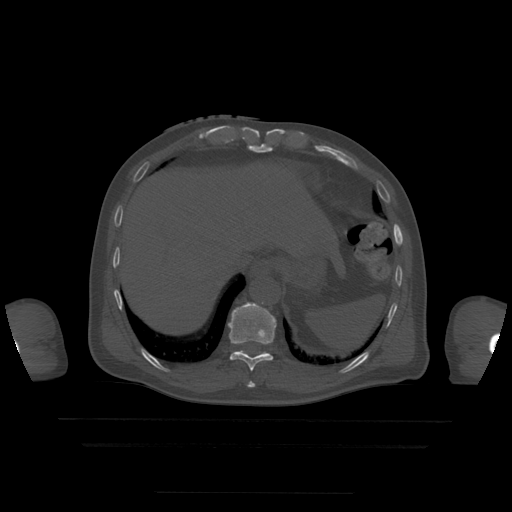
CT including the spine, one axial slice; slice 238 of 522 in the series (ordered by position); bone window (W 1800 / L 400 HU); 512 × 512 image matrix. Patient age 68 years. Case-level facts recorded for this patient, not image findings: primary cancer: urothelial.
Annotated regions visible in this slice (semi-automatic segmentation, software-assisted and operator-edited):
- T10 vertebra: bounding box [x1, y1, x2, y2] px = [228, 302, 277, 372]
- T9 vertebra: [248, 382, 255, 388]